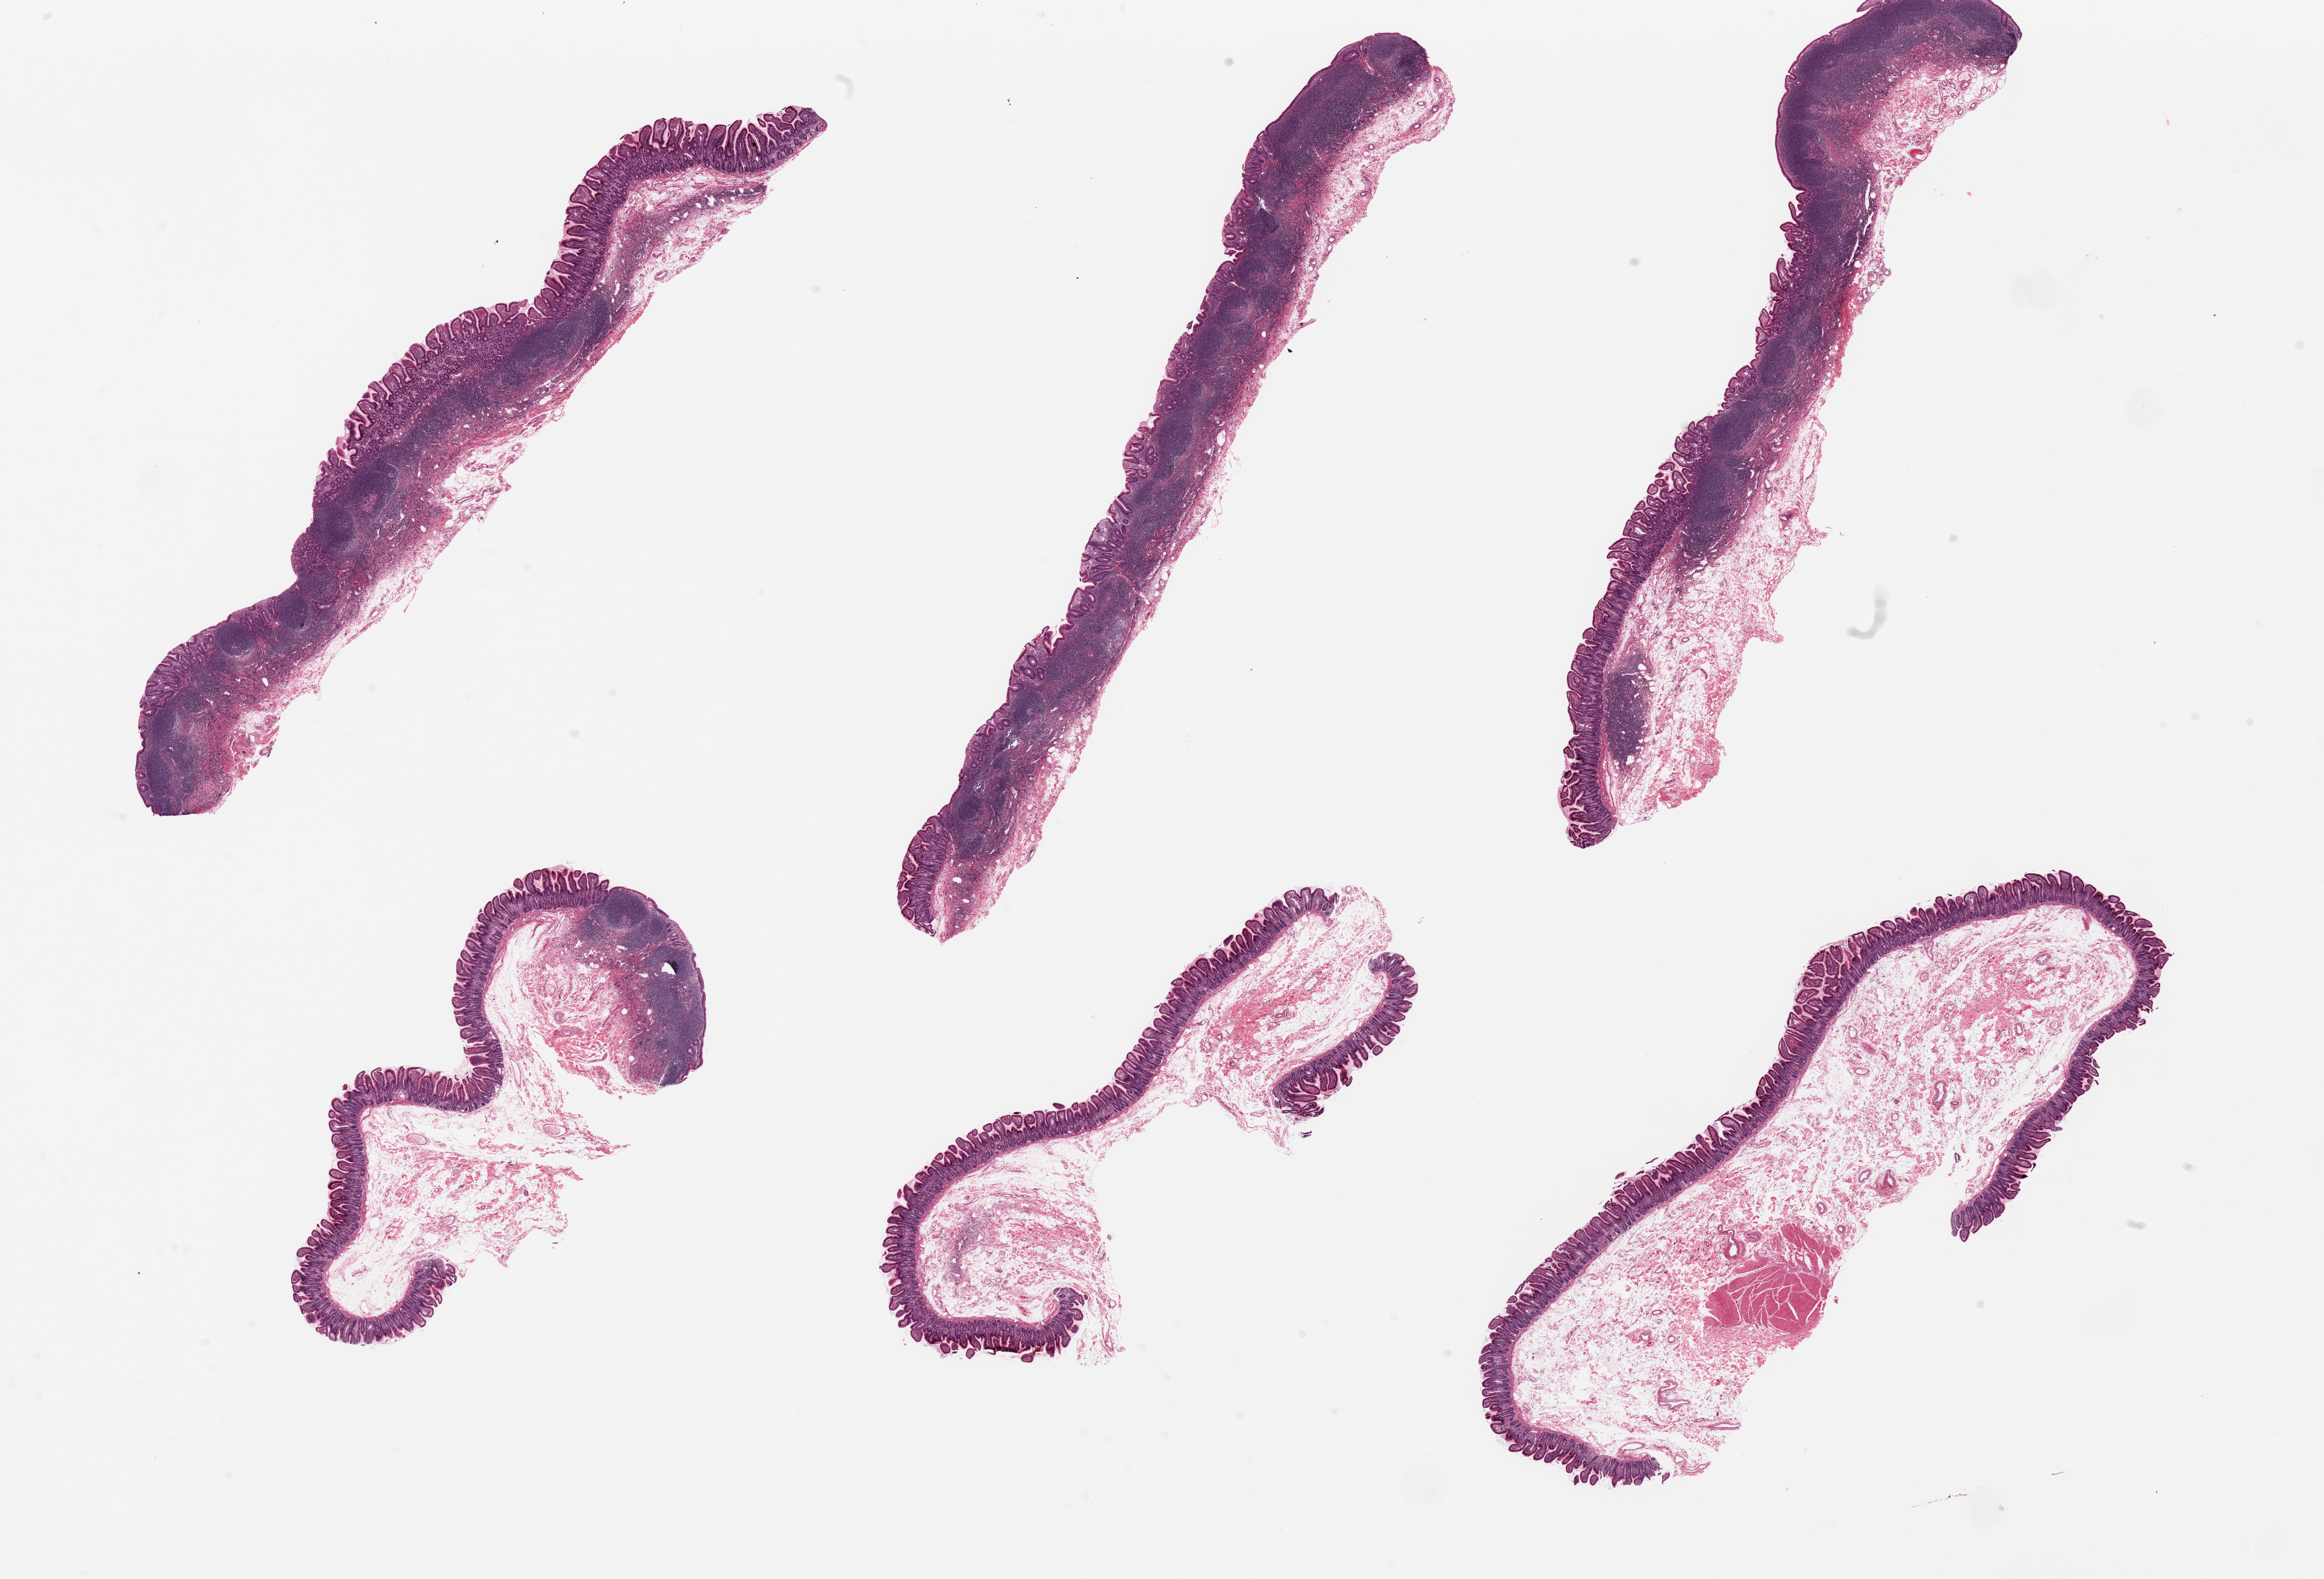
Digitized hematoxylin and eosin (H&E)-stained section, brightfield — a low-resolution overview of the entire scanned area, about 30.5 x 20.7 mm; PAXgene-fixed paraffin-embedded (PFPE) section; sampled site (target tissue): ileum; donor tissue sample. Male donor.
- reviewer comment on this tissue sample: 6 pieces, prominent lymphoid component in 4 of 6 pieces